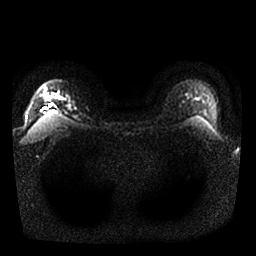
Breast MRI, one axial slice. Position 22 of 25 along the scan axis. Diffusion-weighted series; image 2 of 4 stored at this slice position (different b-values; order by instance number). 1.5 T. 4 mm slice thickness. 256 × 256 image matrix, field of view 340 × 340 mm. Female patient.
Annotated regions visible in this slice (expert manual segmentation):
- tumour on diffusion-weighted imaging: bounding box (x1, y1, x2, y2) in pixels: (45, 93, 49, 96)